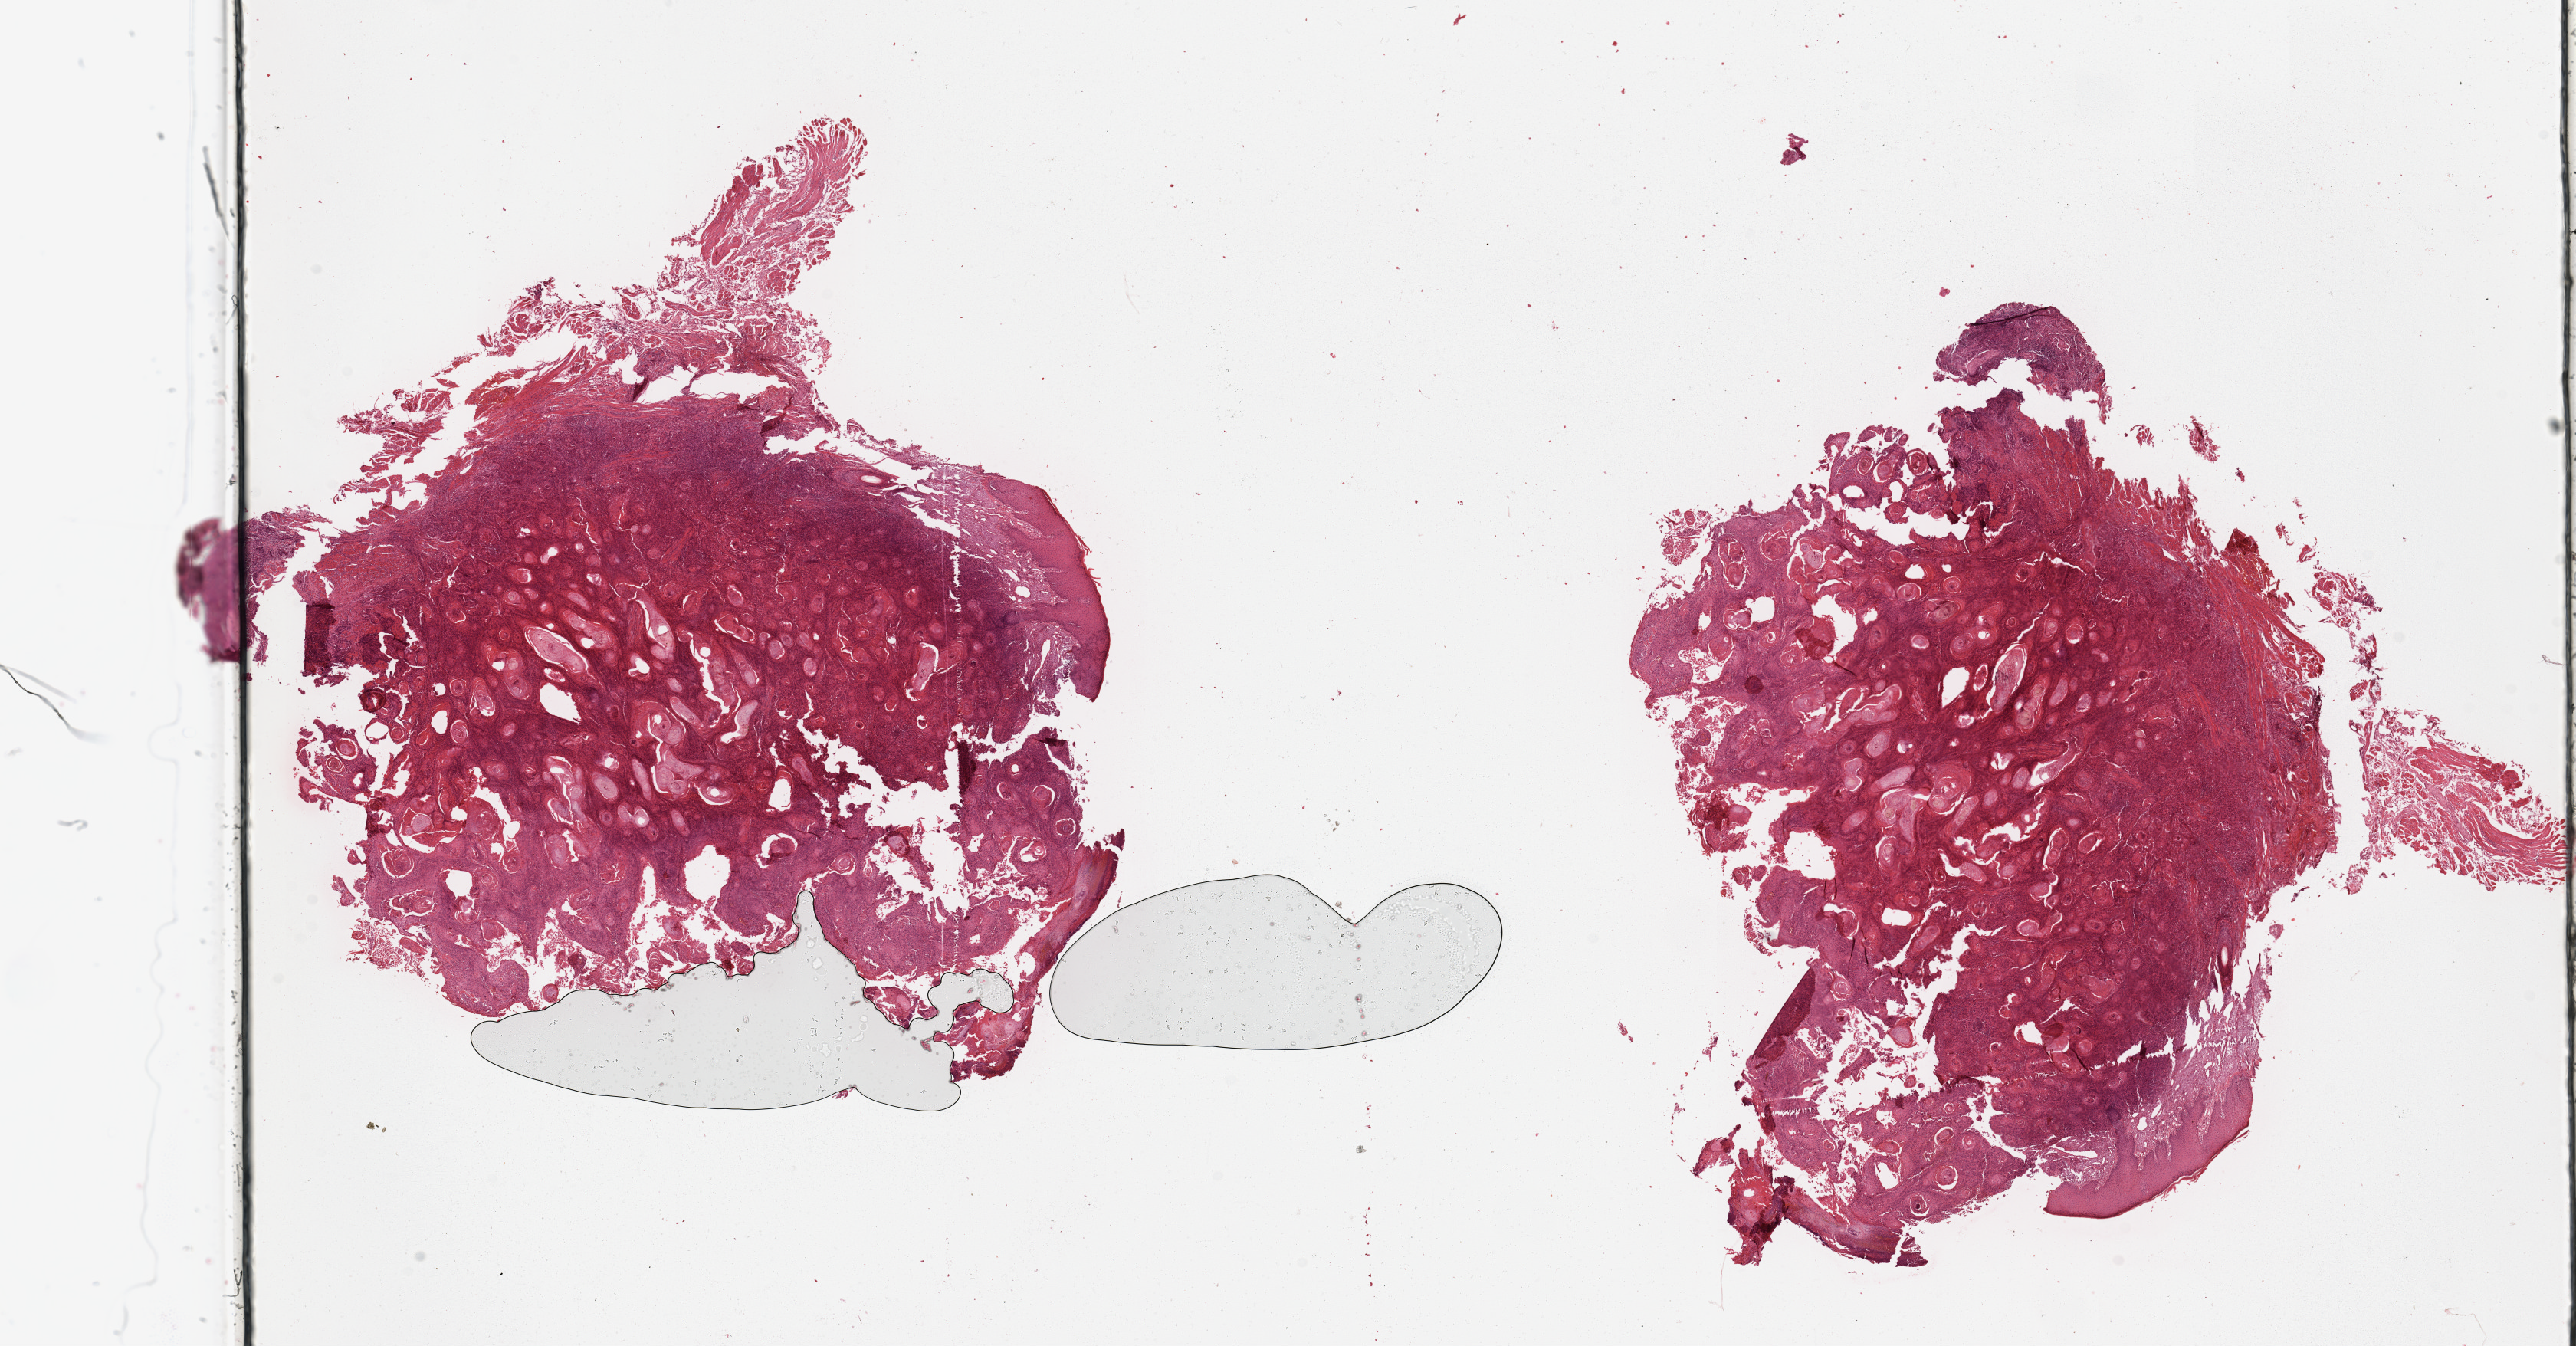
Digitized H&E tissue section (whole slide), shown as a low-resolution overview of the whole scanned area (about 26.6 x 13.9 mm, slide scanned at 20x); head and neck, tissue type not recorded. Female, 80 y/o.
Patient diagnosis: Squamous cell carcinoma, NOS (lip, NOS).